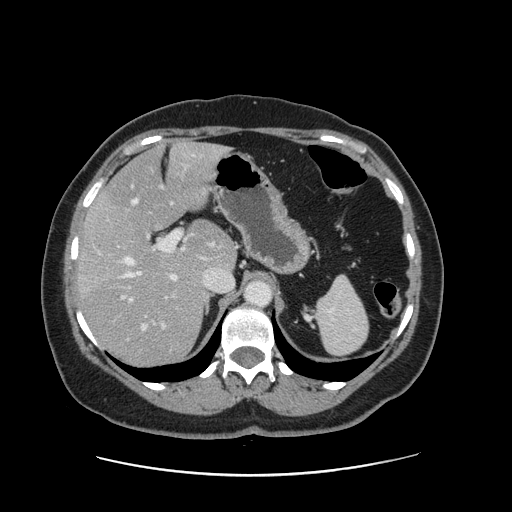
Contrast-enhanced abdominal CT, one axial slice; slice 98 of 161 in the series (ordered by position); 120 kVp; soft-tissue window (W 400 / L 40 HU); 2.5 mm slice thickness; 512 × 512 image matrix, field of view 398 × 398 mm. Female patient, age 62 years. From the clinical record (not read from this slice): diagnosis: colorectal cancer liver metastases, imaged before liver resection; multiple liver metastases: no; largest metastasis: 2.5 cm; chemotherapy before resection: yes.
Outlined on this slice (manually delineated by an expert):
- hepatic veins: bounding box (x1, y1, x2, y2) in pixels: (123, 165, 233, 329)
- liver: (79, 143, 236, 365)
- planned liver remnant (the part of the liver to remain after resection): (103, 143, 235, 269)
- portal vein (with intrahepatic branches): (128, 230, 194, 329)